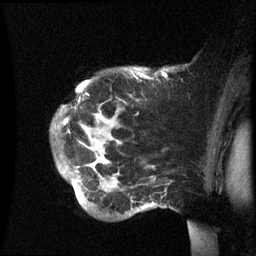
Breast MRI (dynamic contrast-enhanced), one sagittal slice. Position 47 of 60 along the scan axis. Dynamic contrast-enhanced series, image 2 of 3 at this slice position (ordered by acquisition). 1.5 T. TE 4.2 ms, TR 8.4 ms. 2.4 mm slice thickness. 256 × 256 image matrix, field of view 230 × 230 mm. Female patient, age 49 years.
Outlined on this slice (semi-automatic segmentation, software-assisted and operator-edited):
- analysis volume of interest (the breast-tissue region the enhancement analysis was run in; not a lesion): bounding box (x1, y1, x2, y2) in pixels: (51, 67, 173, 218)
- tumour enhancement mask (voxels above the 70 % enhancement threshold inside the analysis volume of interest): (63, 72, 164, 190)